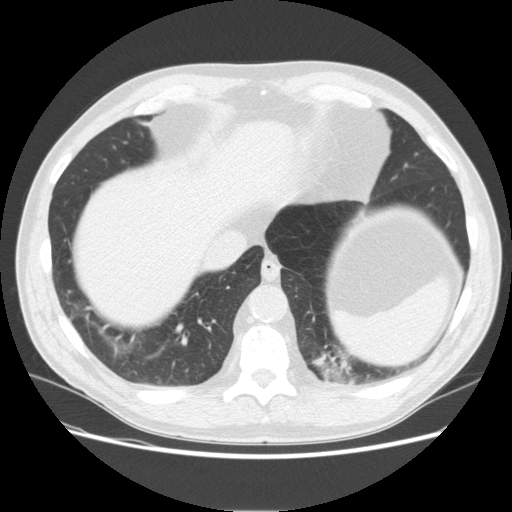
Low-dose screening chest CT, one axial slice. Position 49 of 165 along the scan axis. 120 kVp. Lung window (W 1500 / L -600 HU). 2.5 mm slice thickness. 512 × 512 image matrix, field of view 375 × 375 mm.
Structures marked on this image (manually delineated by an expert):
- lesion 1 (tumor, upper lobe of left lung): box from (x=315, y=350) to (x=357, y=384) px